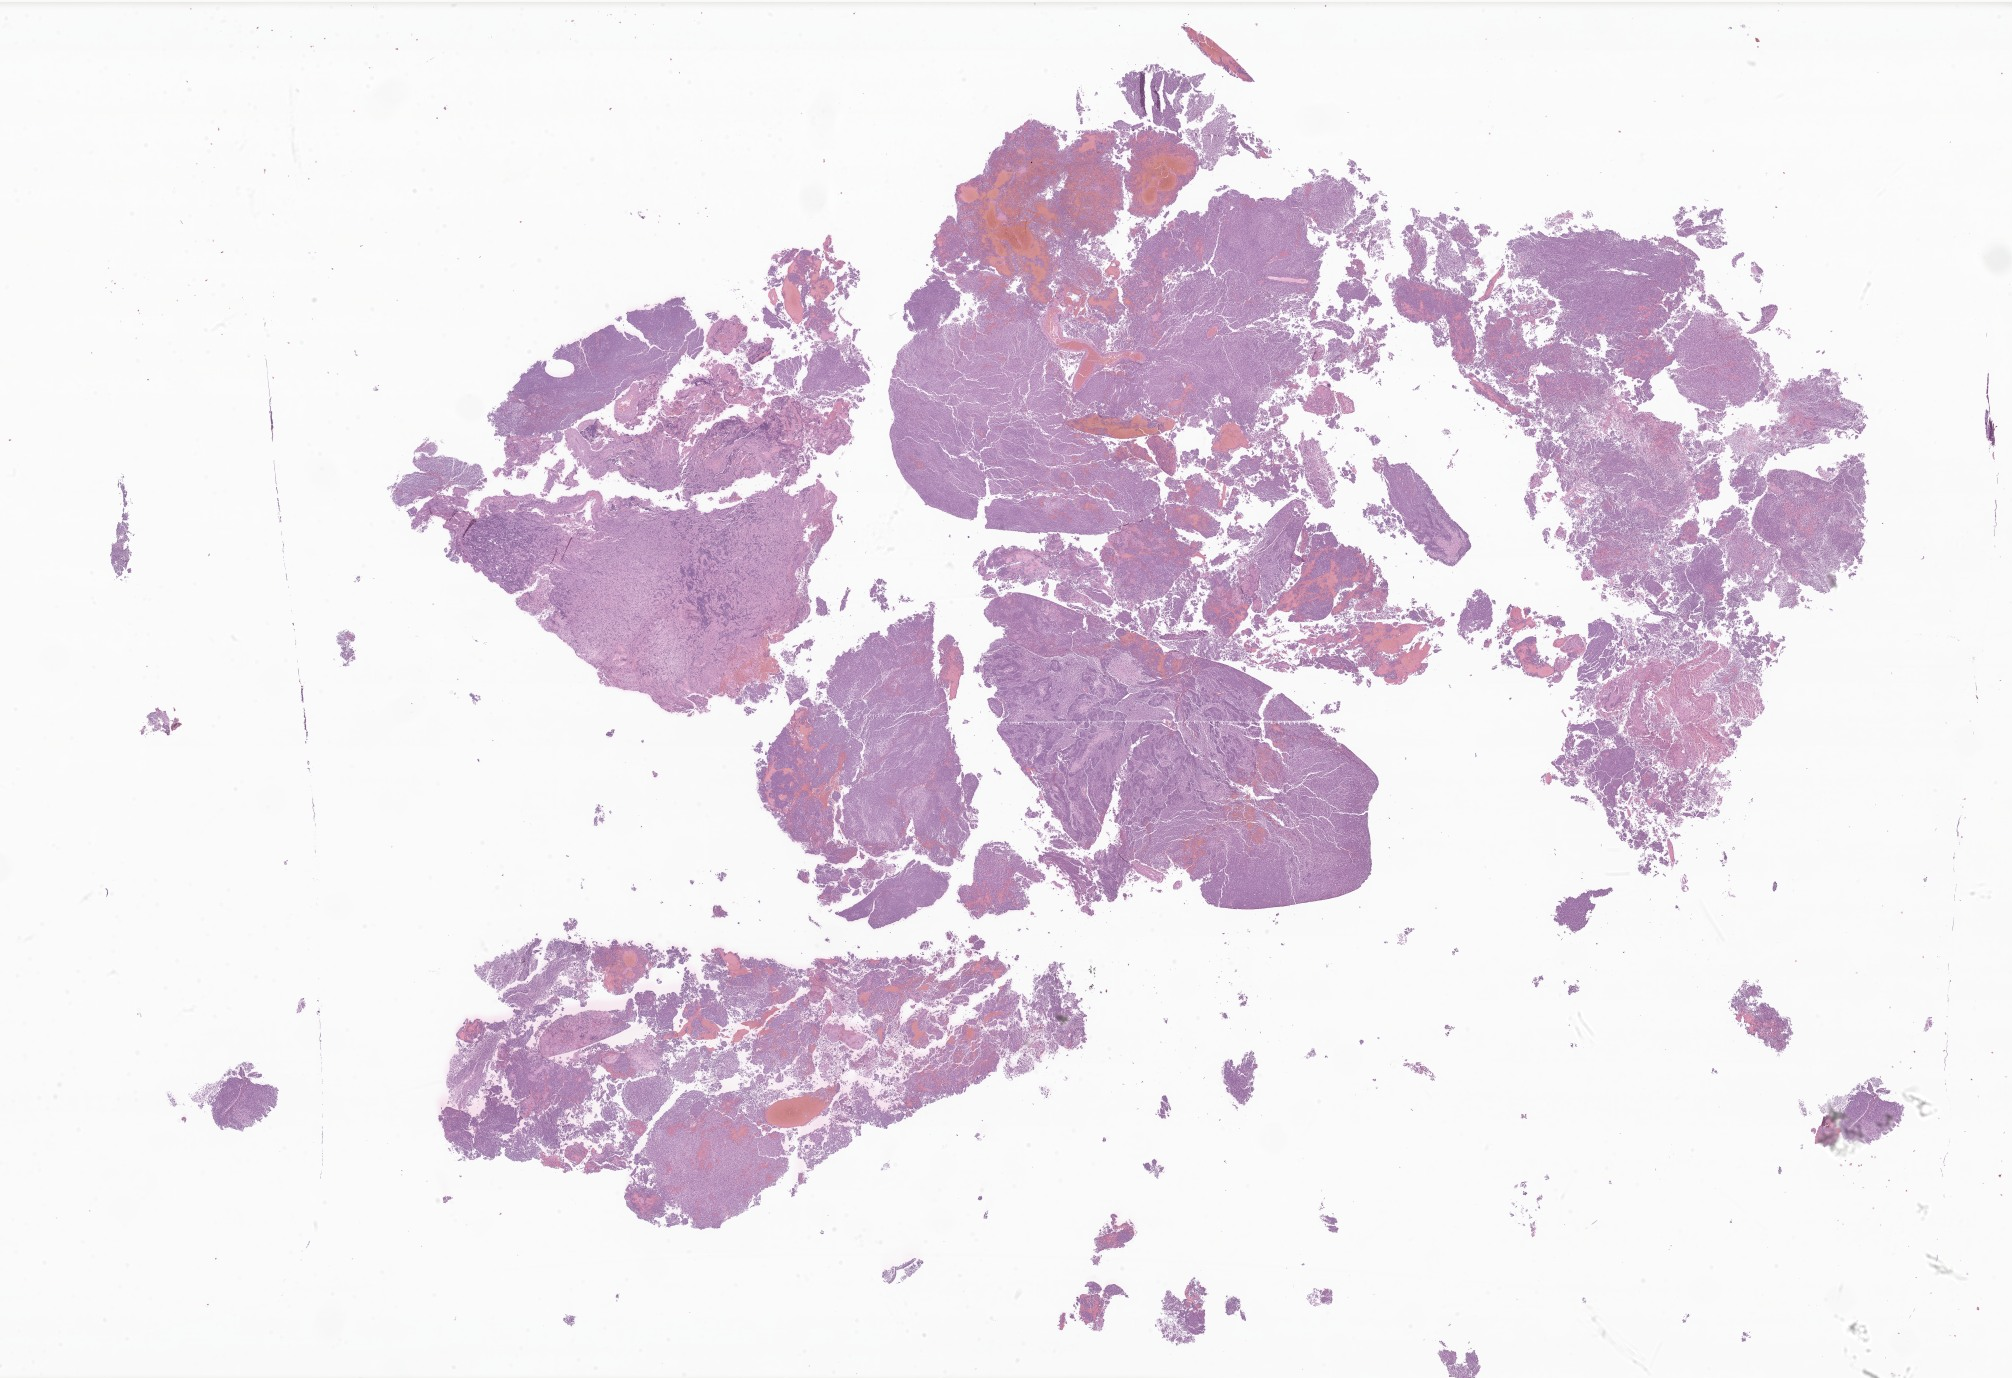
Whole-slide image, hematoxylin and eosin (H&E) stain of tumor tissue from the cerebellum, a low-resolution overview of the entire scanned area, about 33.9 x 23.2 mm; formalin-fixed paraffin-embedded section. Patient: female, age 71 months (5 years 11 months).
* recorded diagnosis: Medulloblastoma, NOS